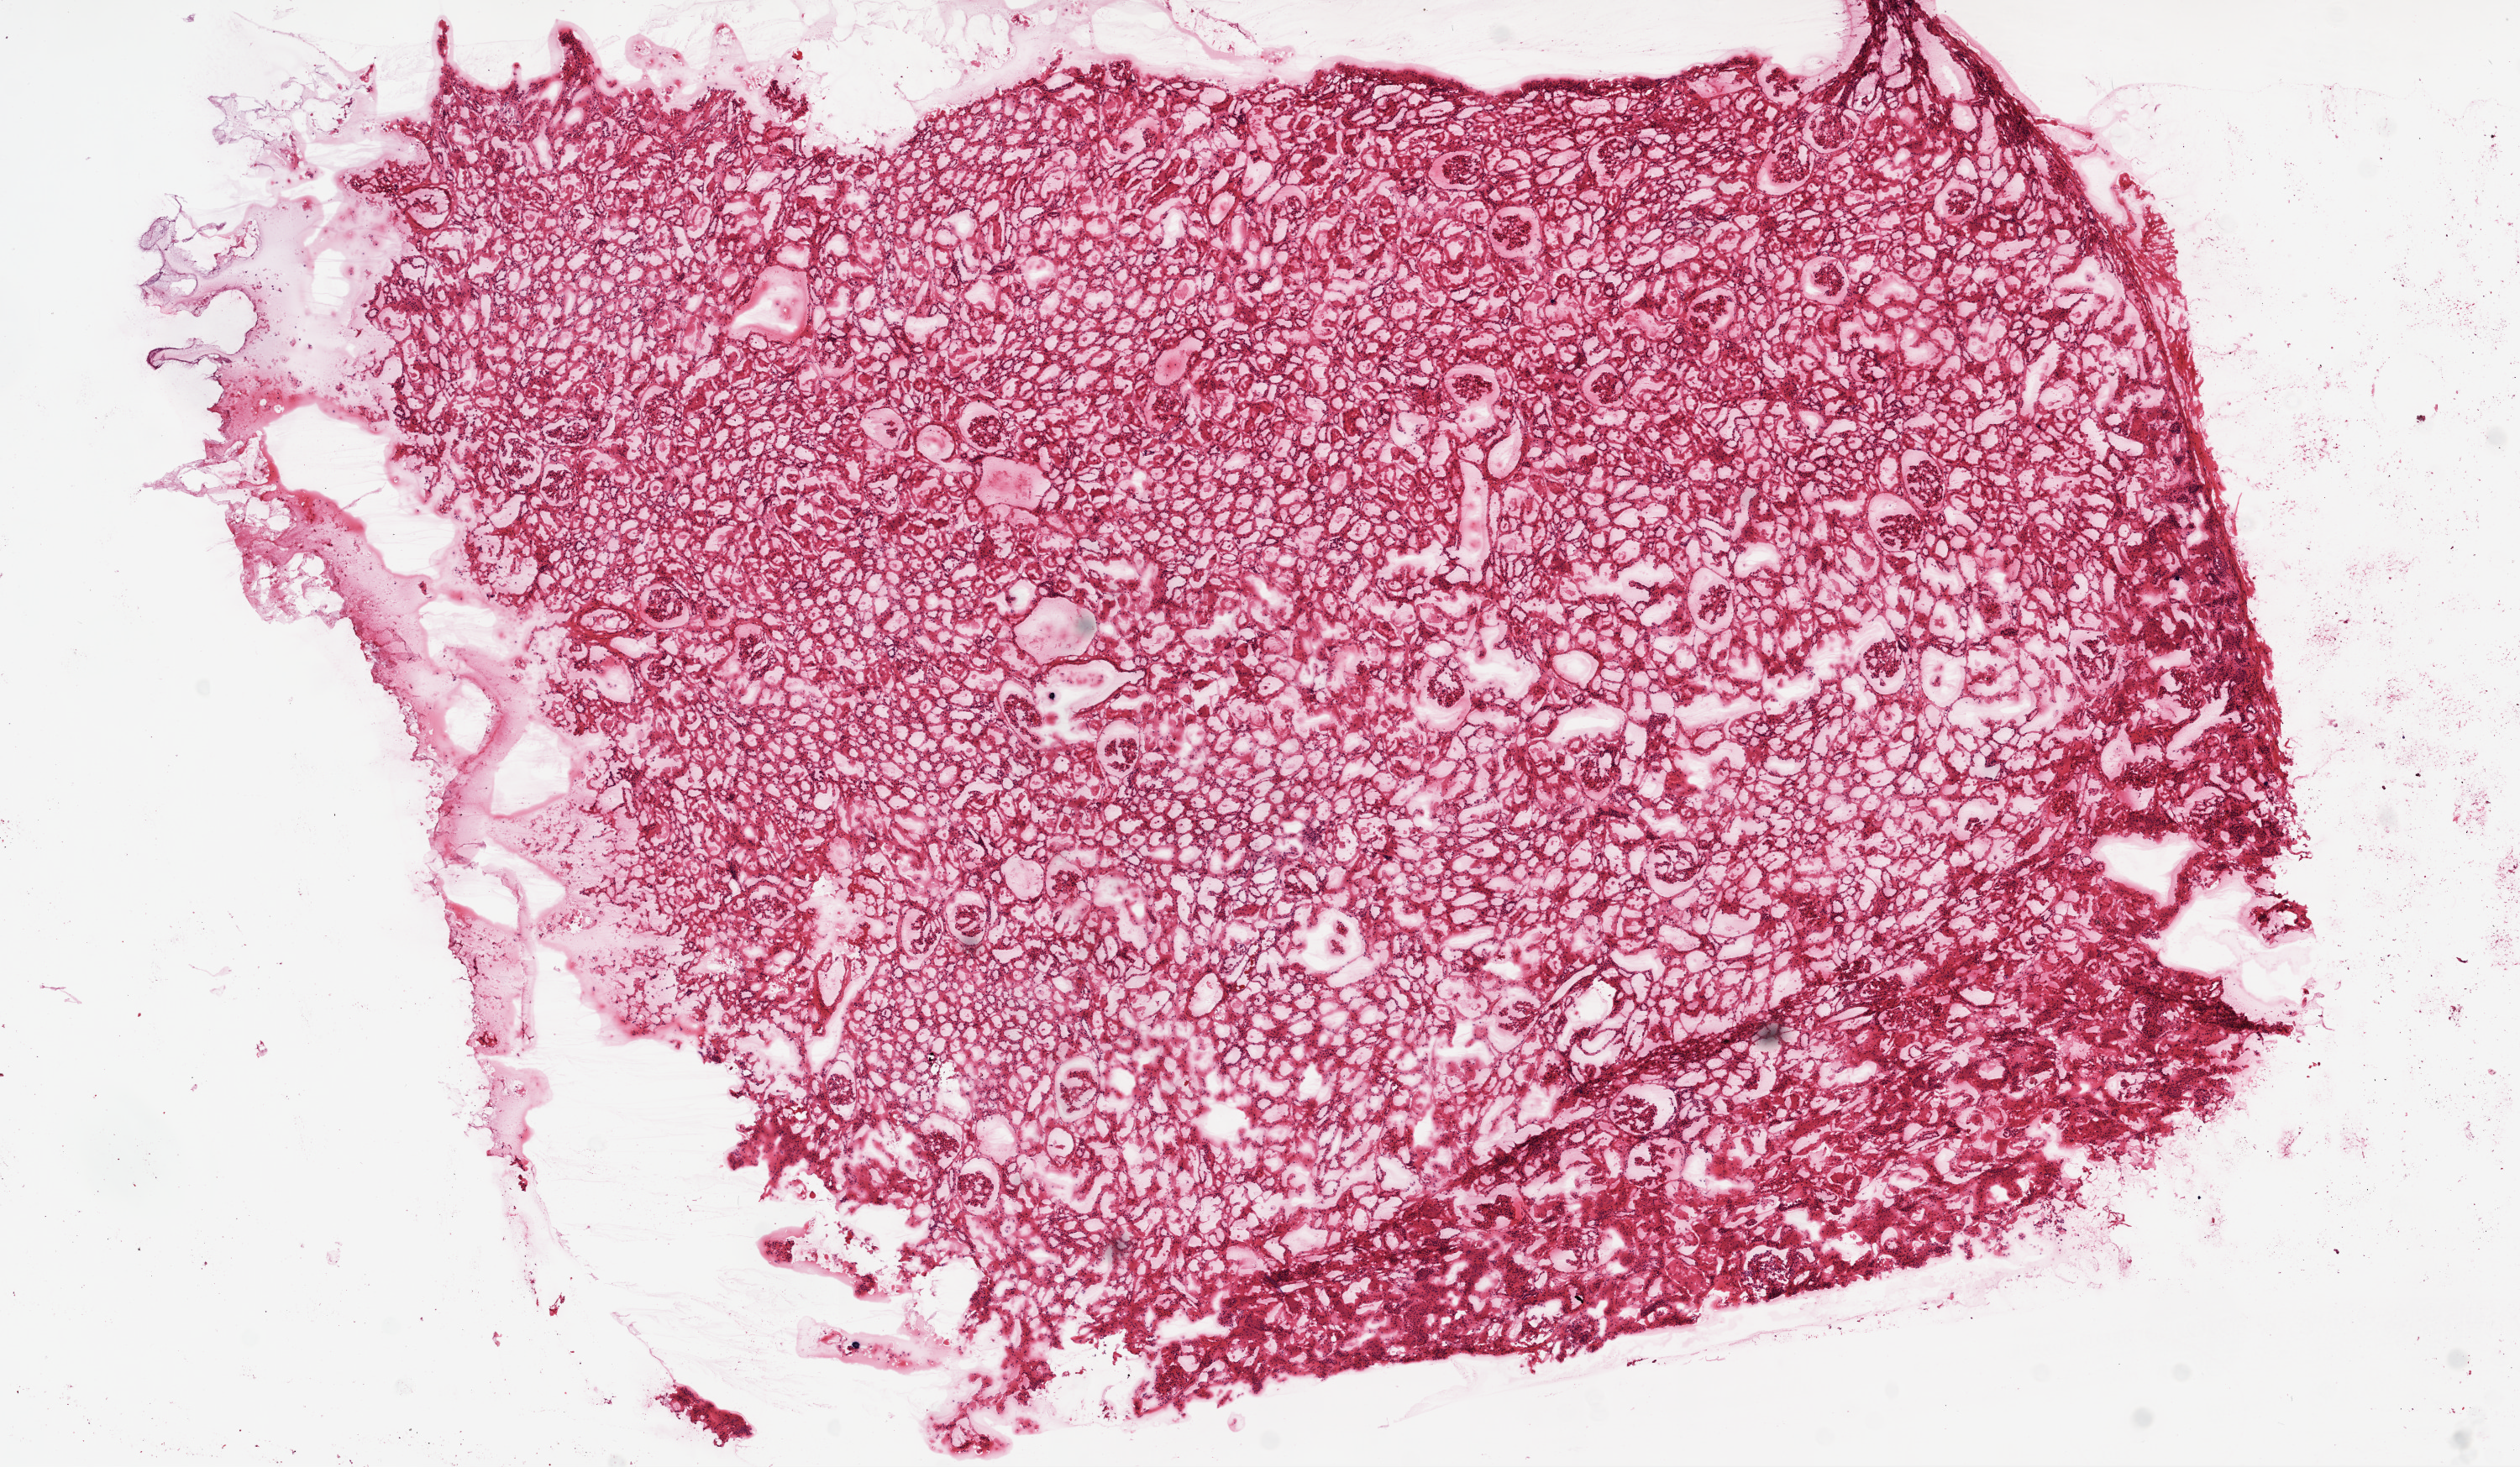
Whole-slide histology image, H&E, whole scanned area (about 12.0 x 7.0 mm, acquisition: 20x scan) shown as a low-resolution overview; frozen section from the top of the tissue portion; solid tissue normal (non-tumour tissue) sample from the kidney. Male, age 33 years at initial diagnosis.
• this section: solid tissue normal (non-tumour) sample from the same patient
• patient diagnosis: Clear cell adenocarcinoma, NOS